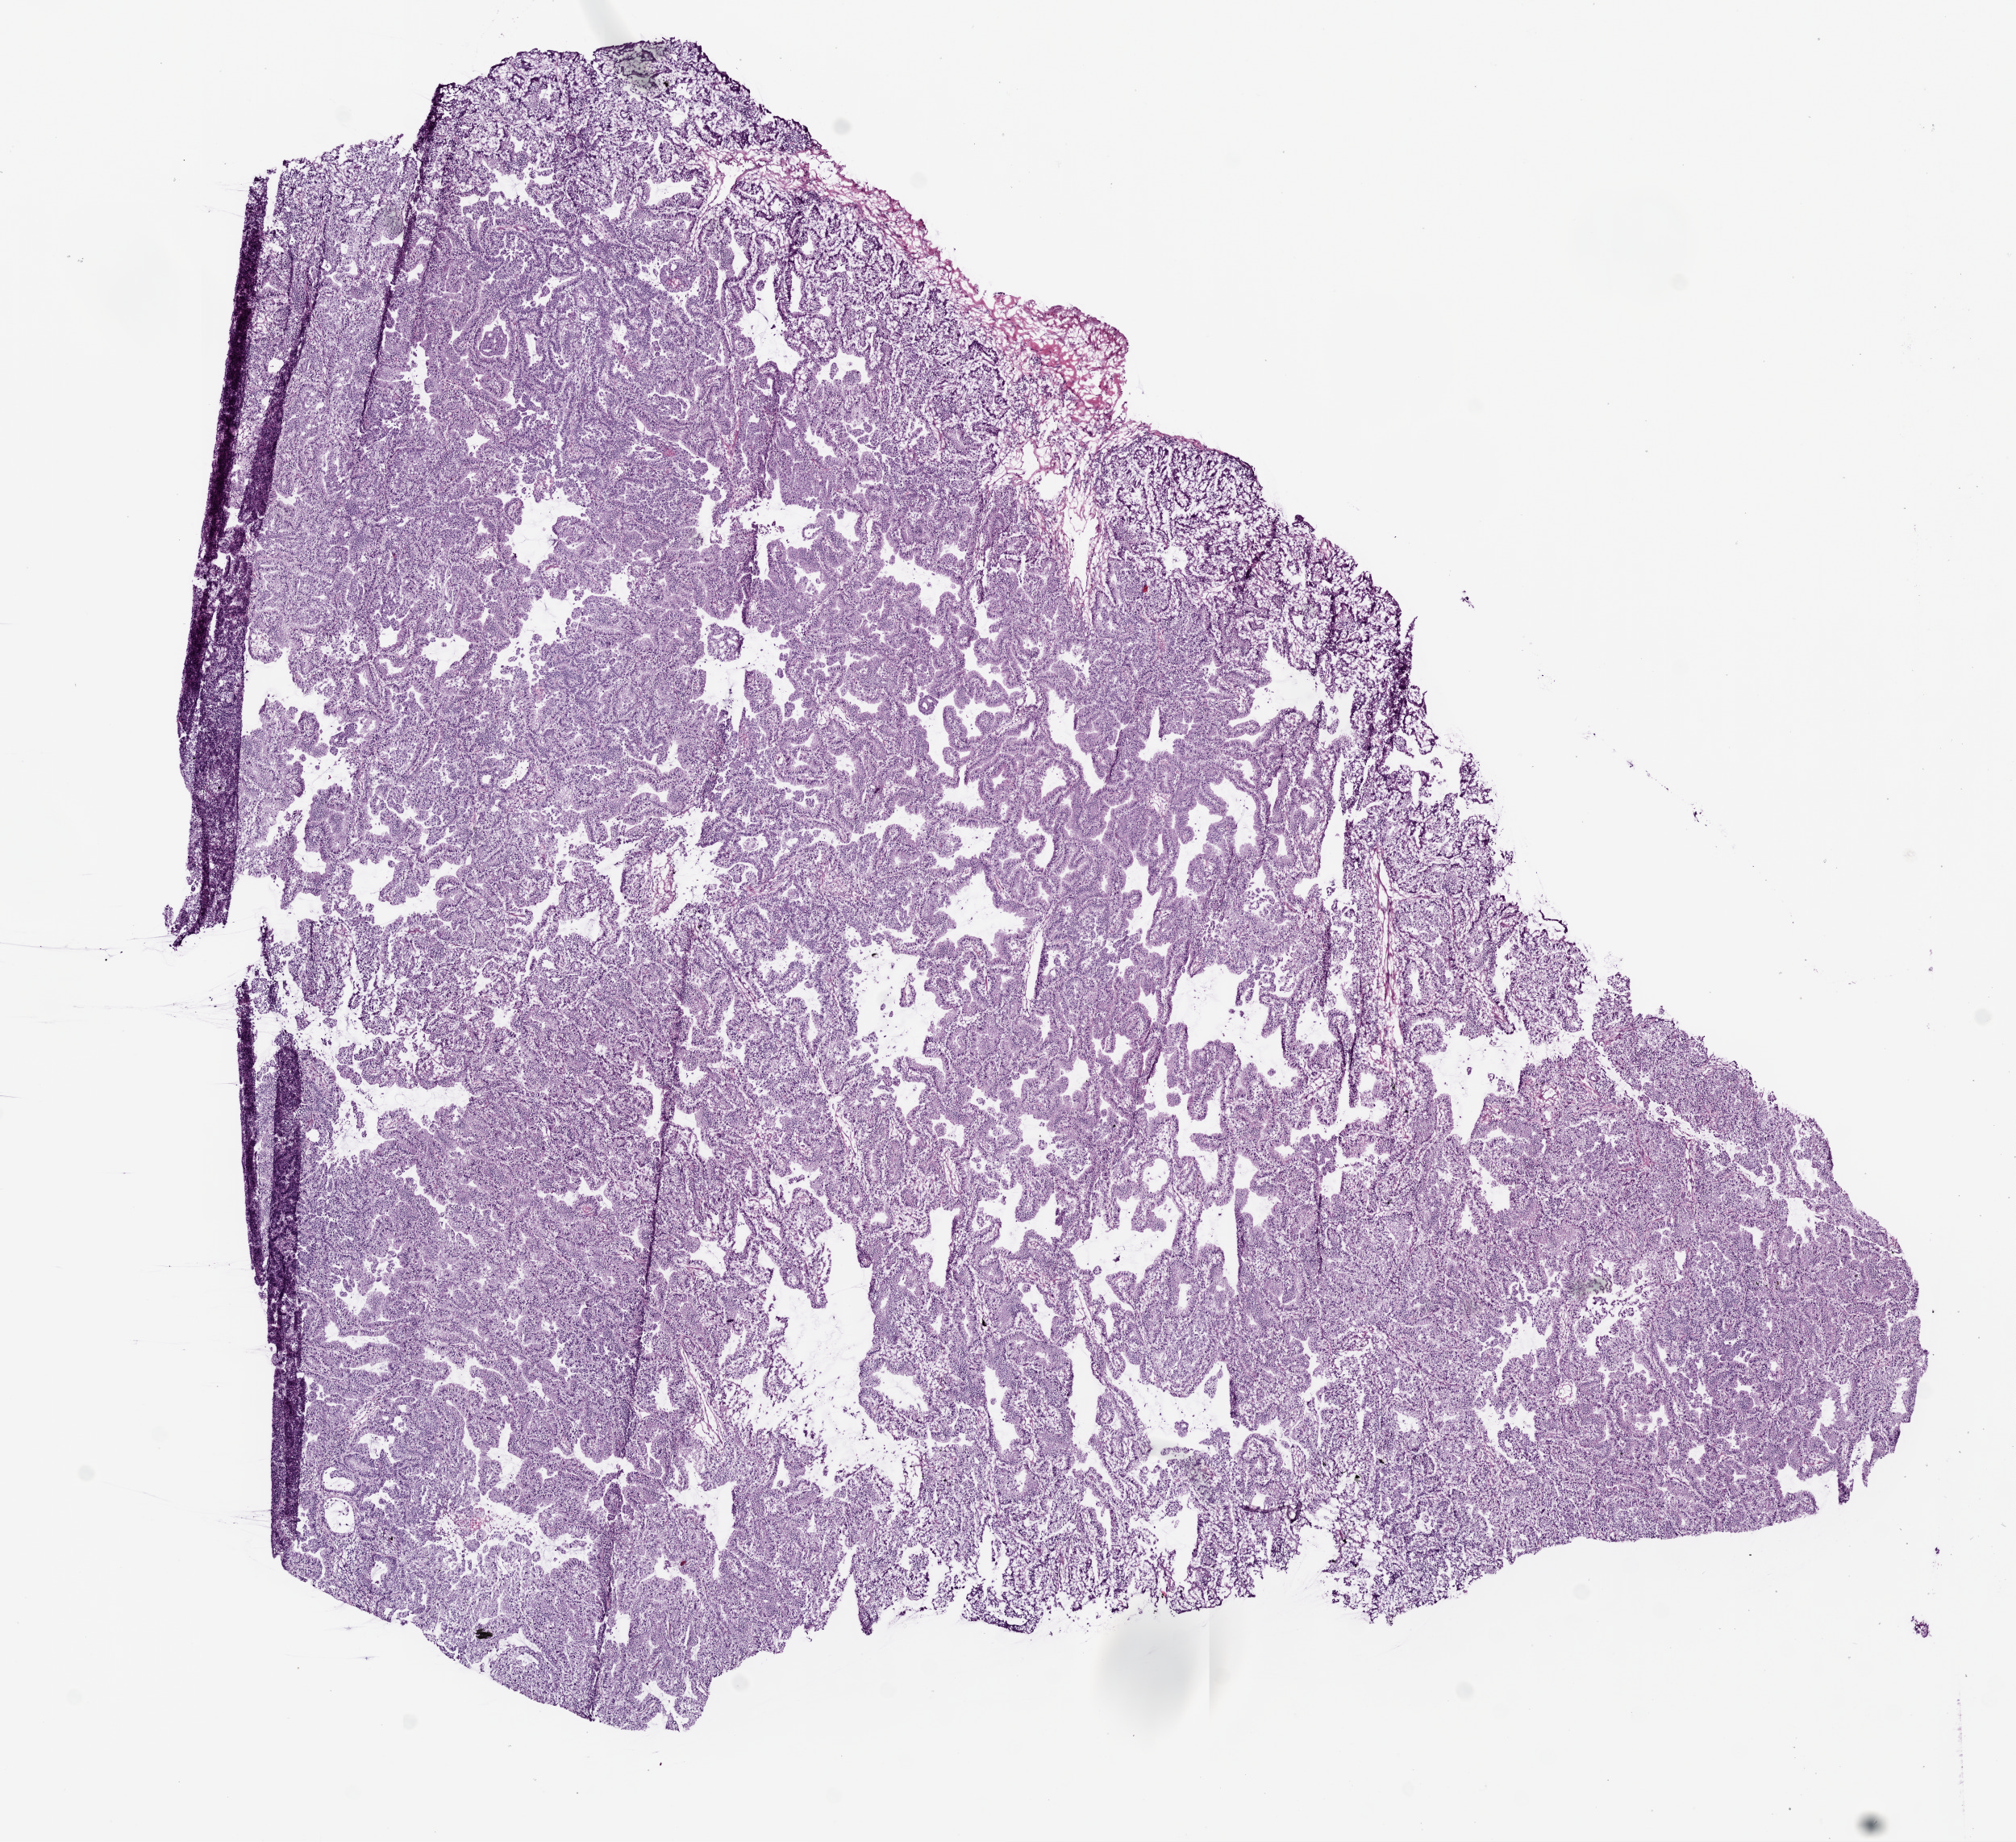
Whole-slide histology image, H&E, shown as a low-resolution overview of the whole scanned area (about 10.0 x 9.2 mm), frozen section from the bottom of the tissue portion, sample: primary tumour, lung. Male, age 76 years at initial diagnosis. Slide review estimates, as recorded: tumour nuclei 75%, normal cells 0%, stromal cells 10%, necrosis 1%.
AJCC pathologic stage: IIIB (5th edition). Diagnosis: Adenocarcinoma with mixed subtypes (lower lobe, lung). TNM: T4 N1 M0.